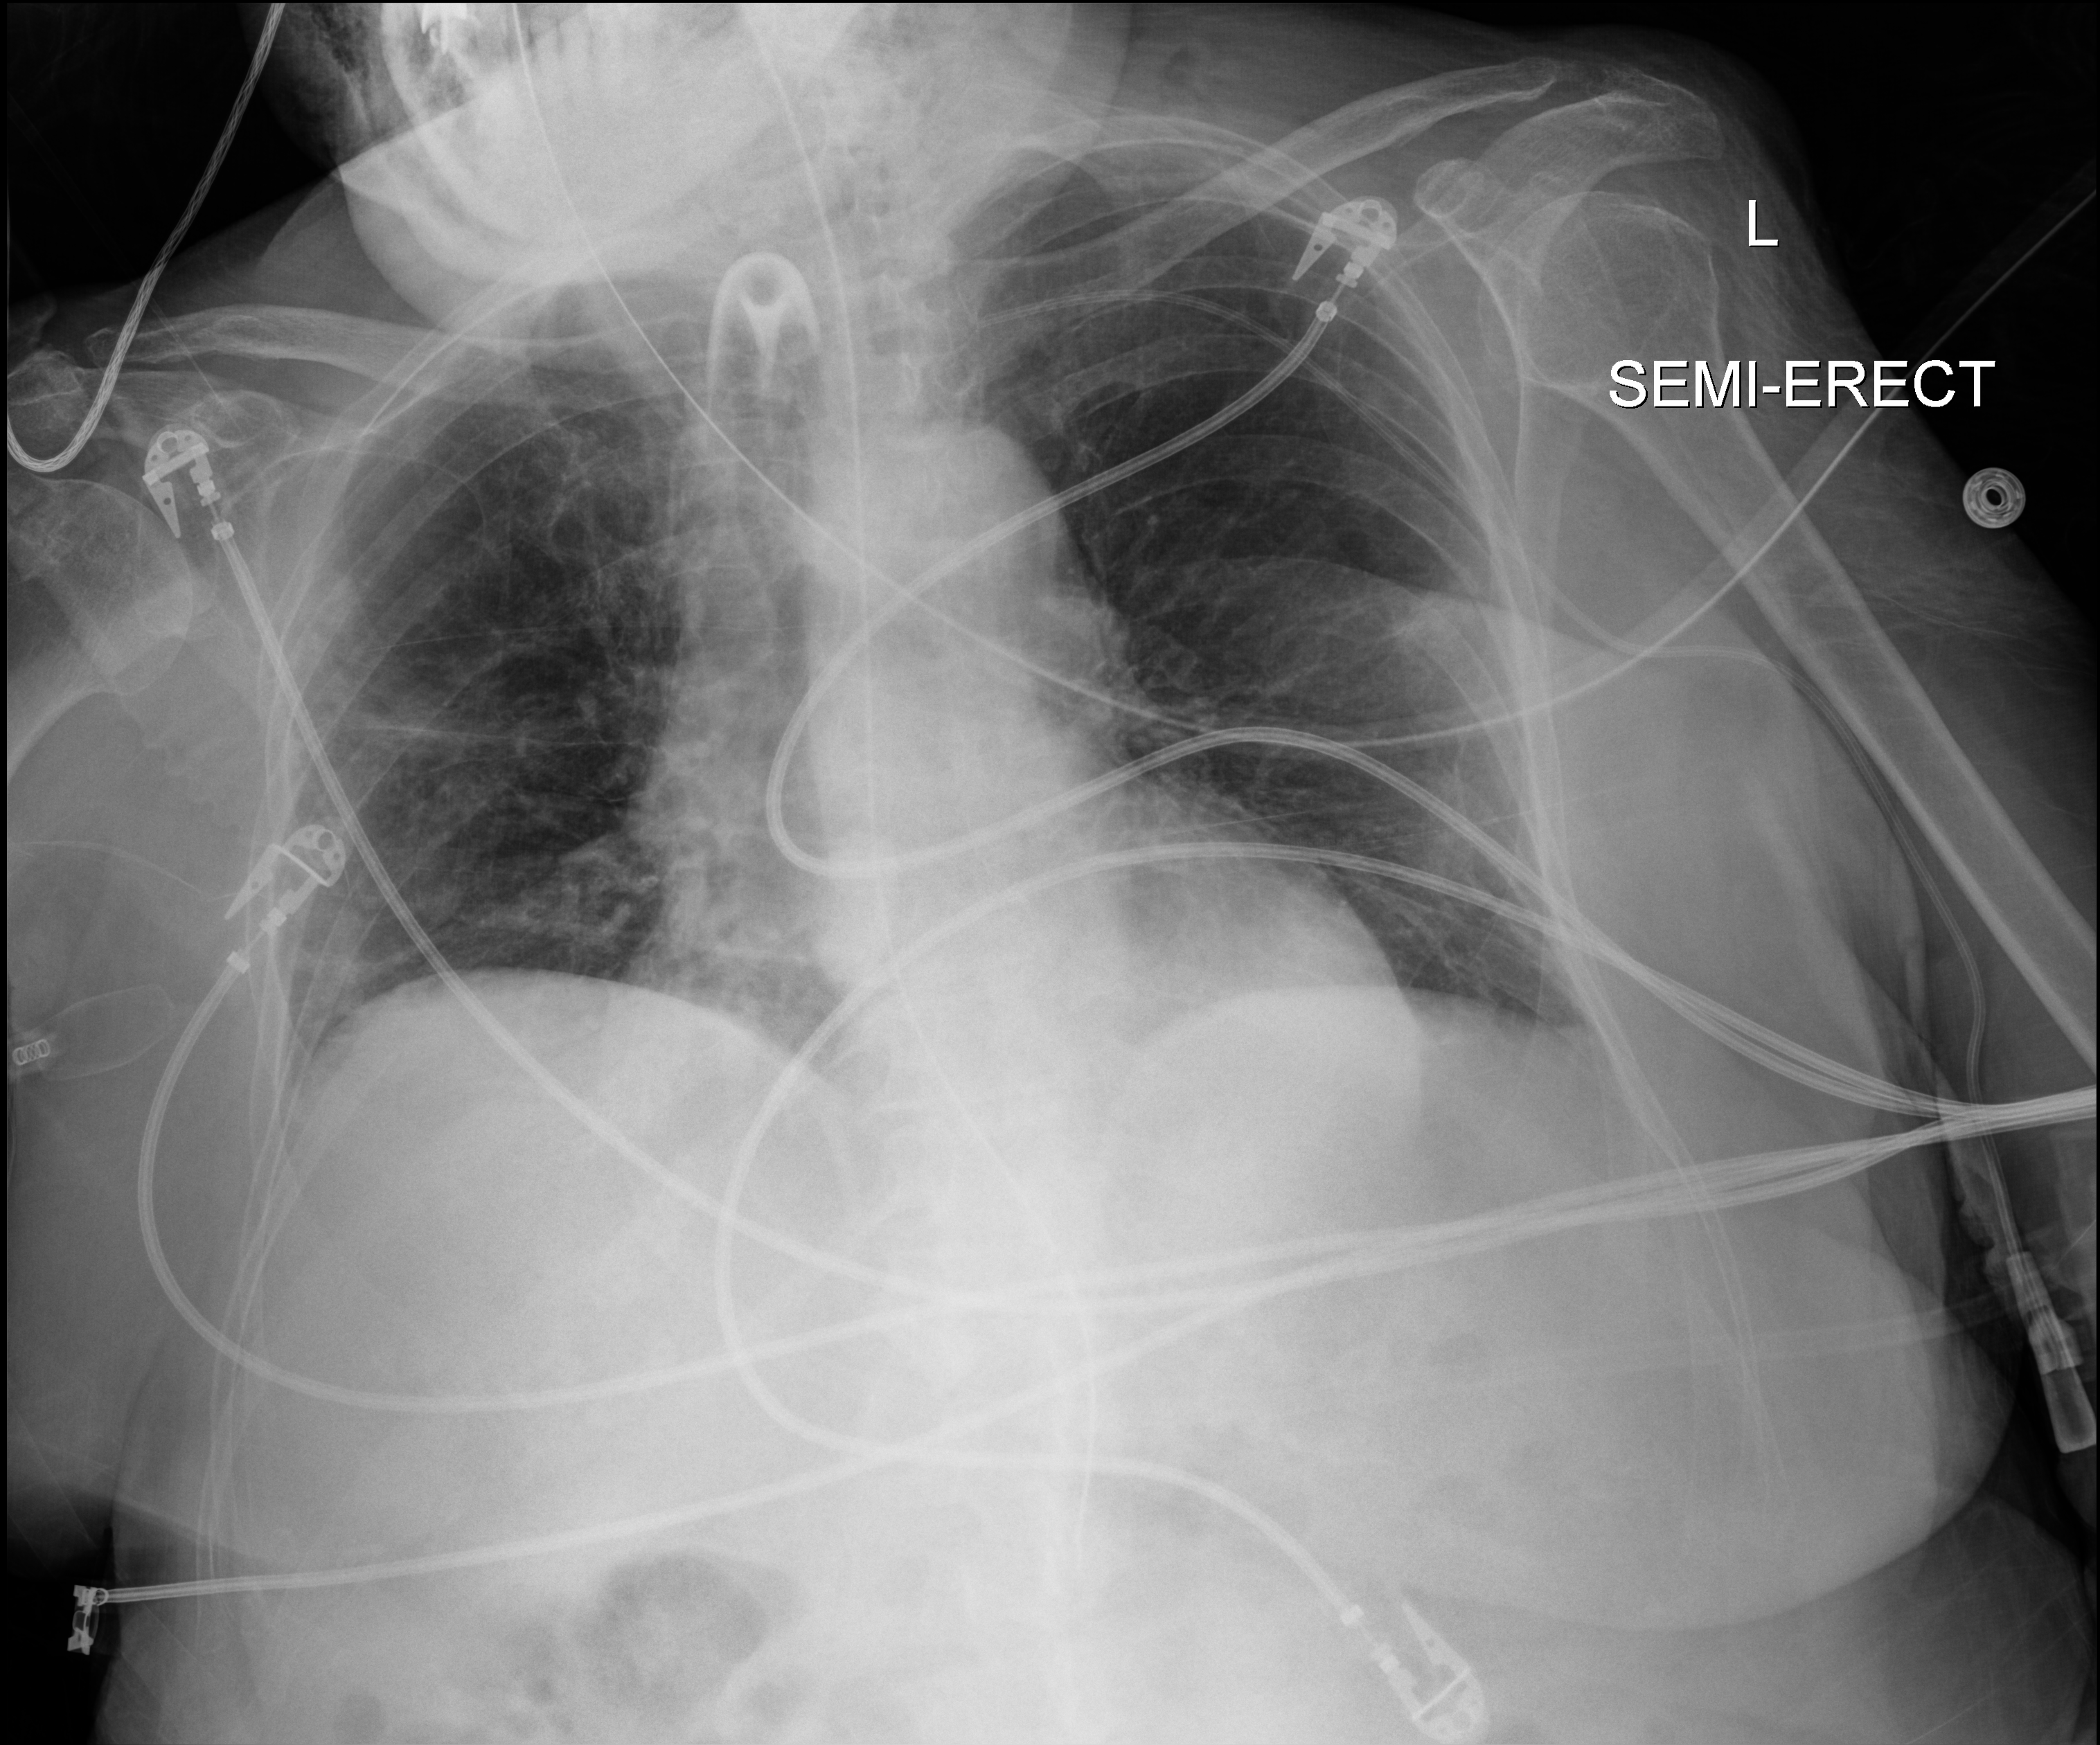
Portable chest radiograph. Patient hospitalised with COVID-19; female, aged 75–90 years.
From the hospital-stay record, not from the radiograph (when in the stay this image was taken is not recorded): COPD (admission record): no; diabetes (admission record): no.